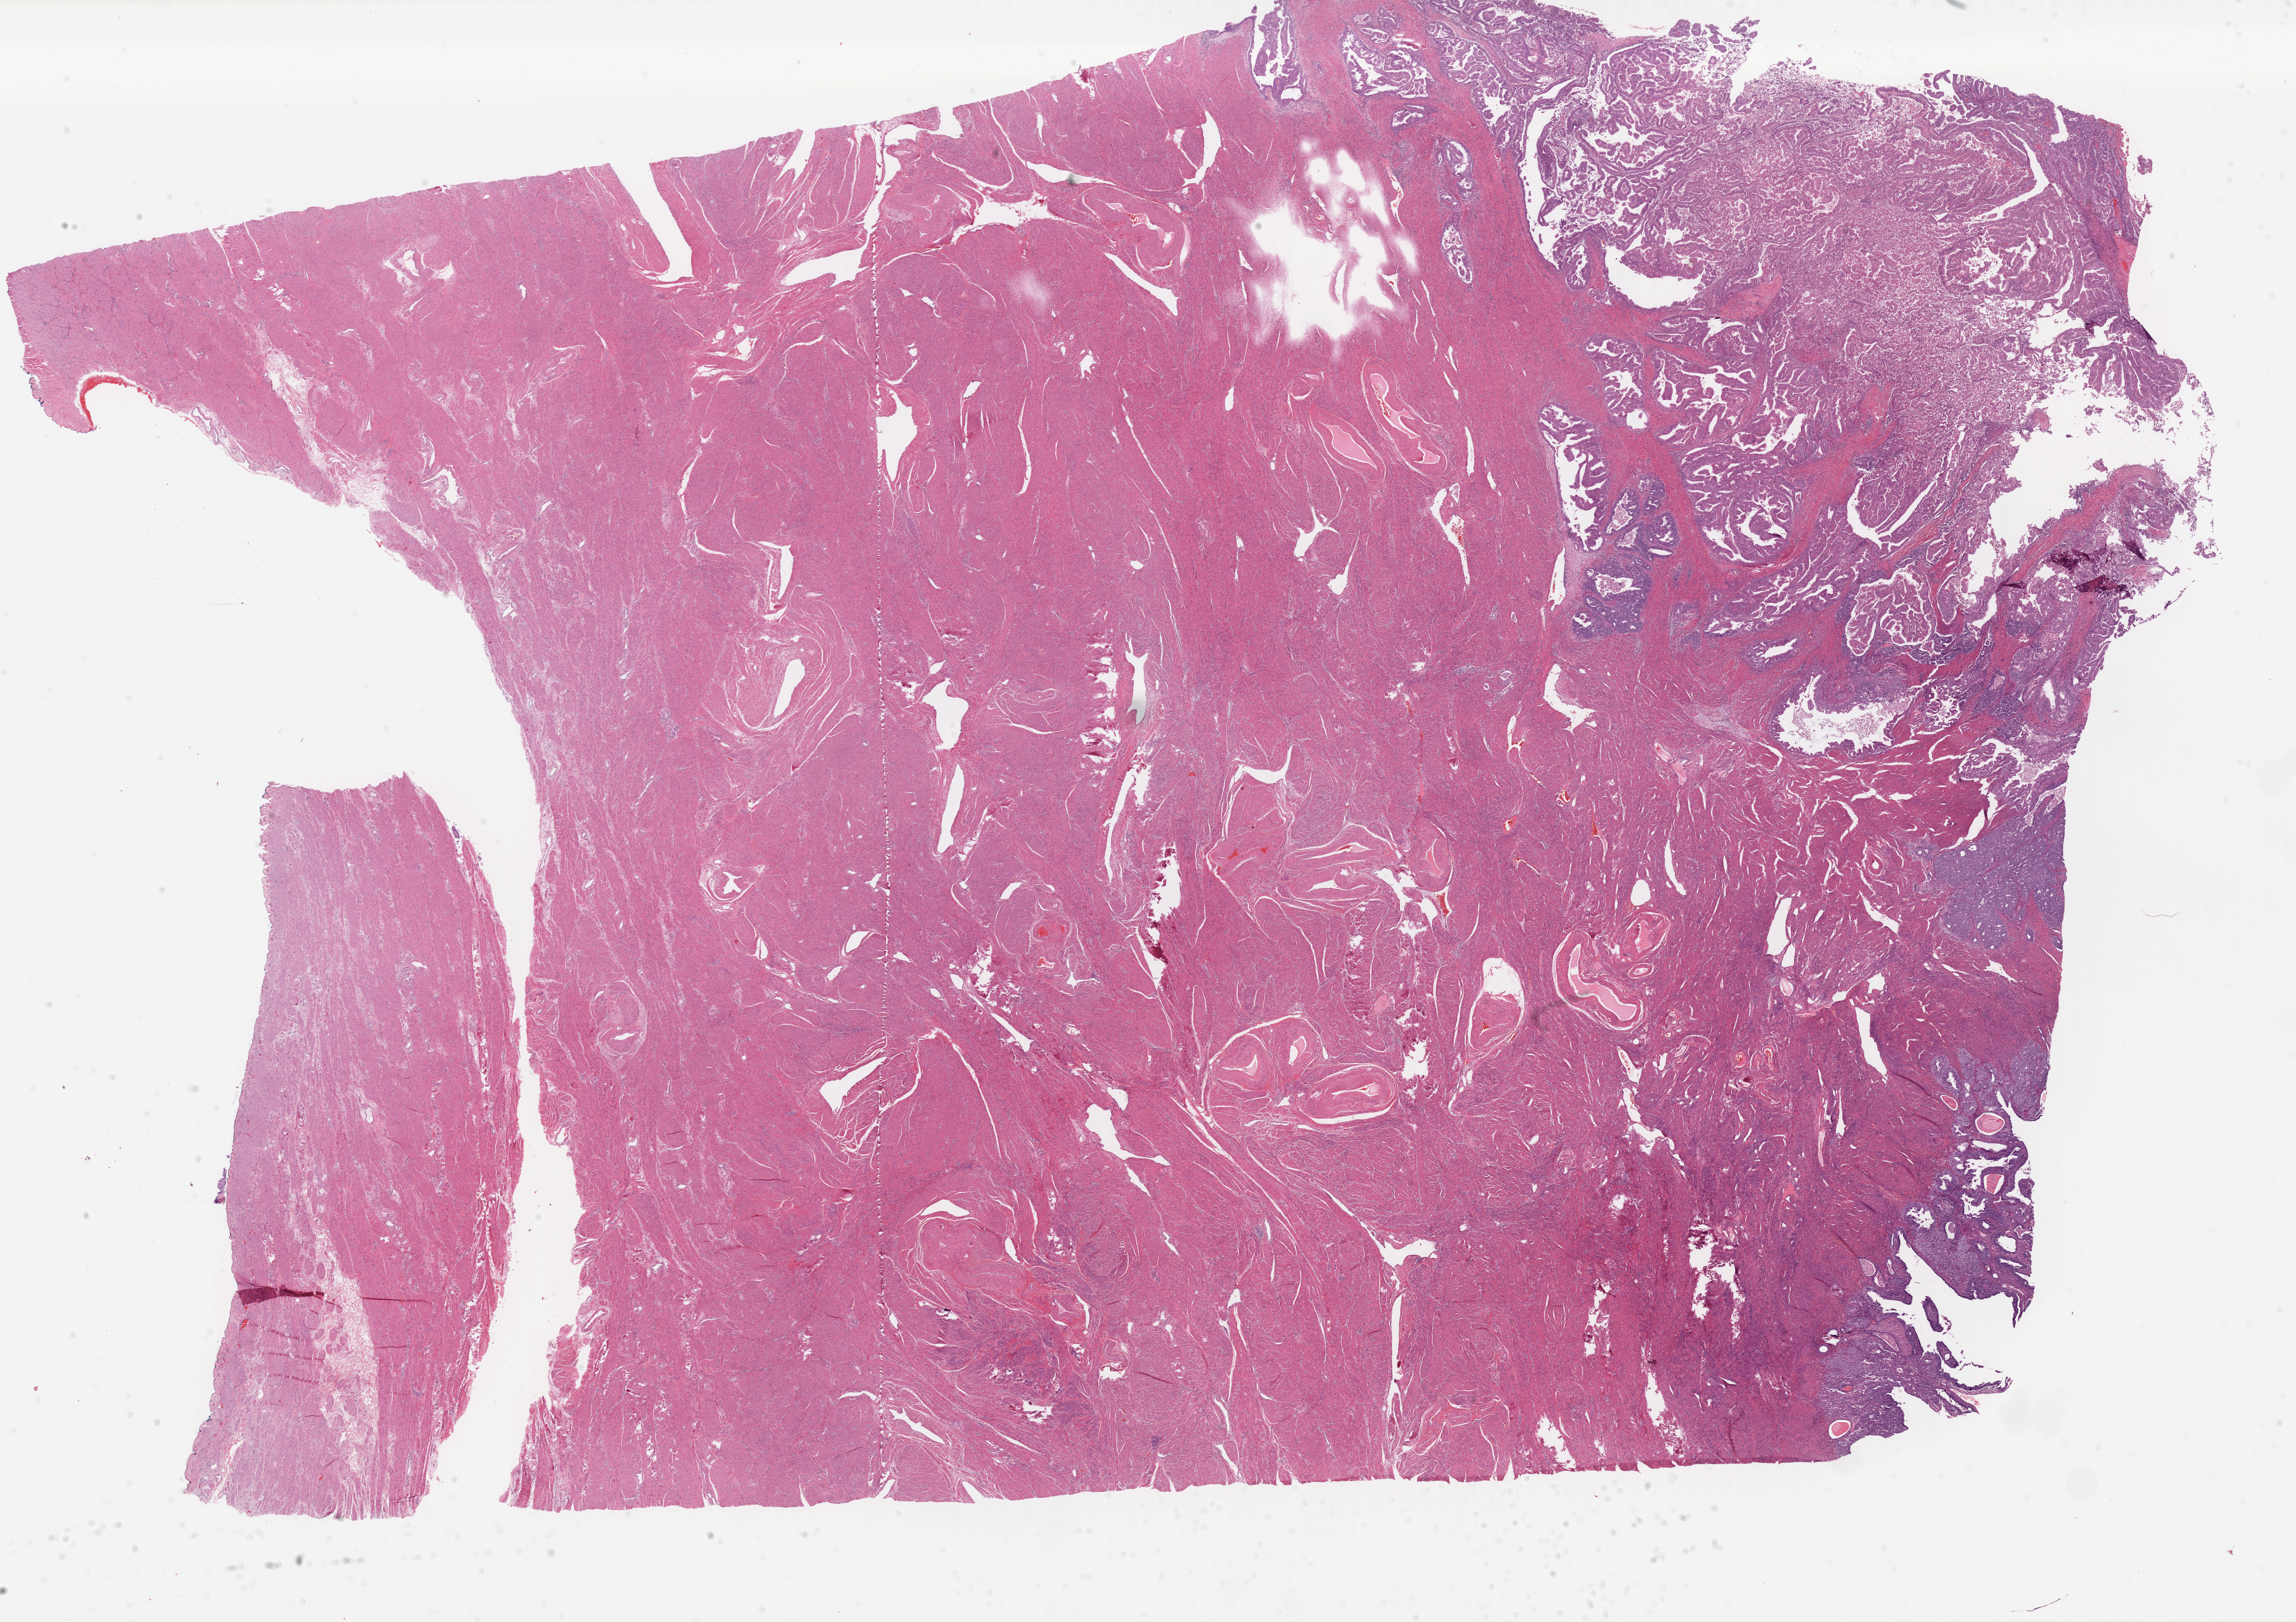
Whole-slide histology image, H&E — low-resolution overview of the scanned area, about 30.8 x 21.7 mm, FFPE section, uterus, primary tumour sample. Patient: female, age at initial diagnosis 53 years.
Diagnosis: Serous cystadenocarcinoma, NOS (endometrium).